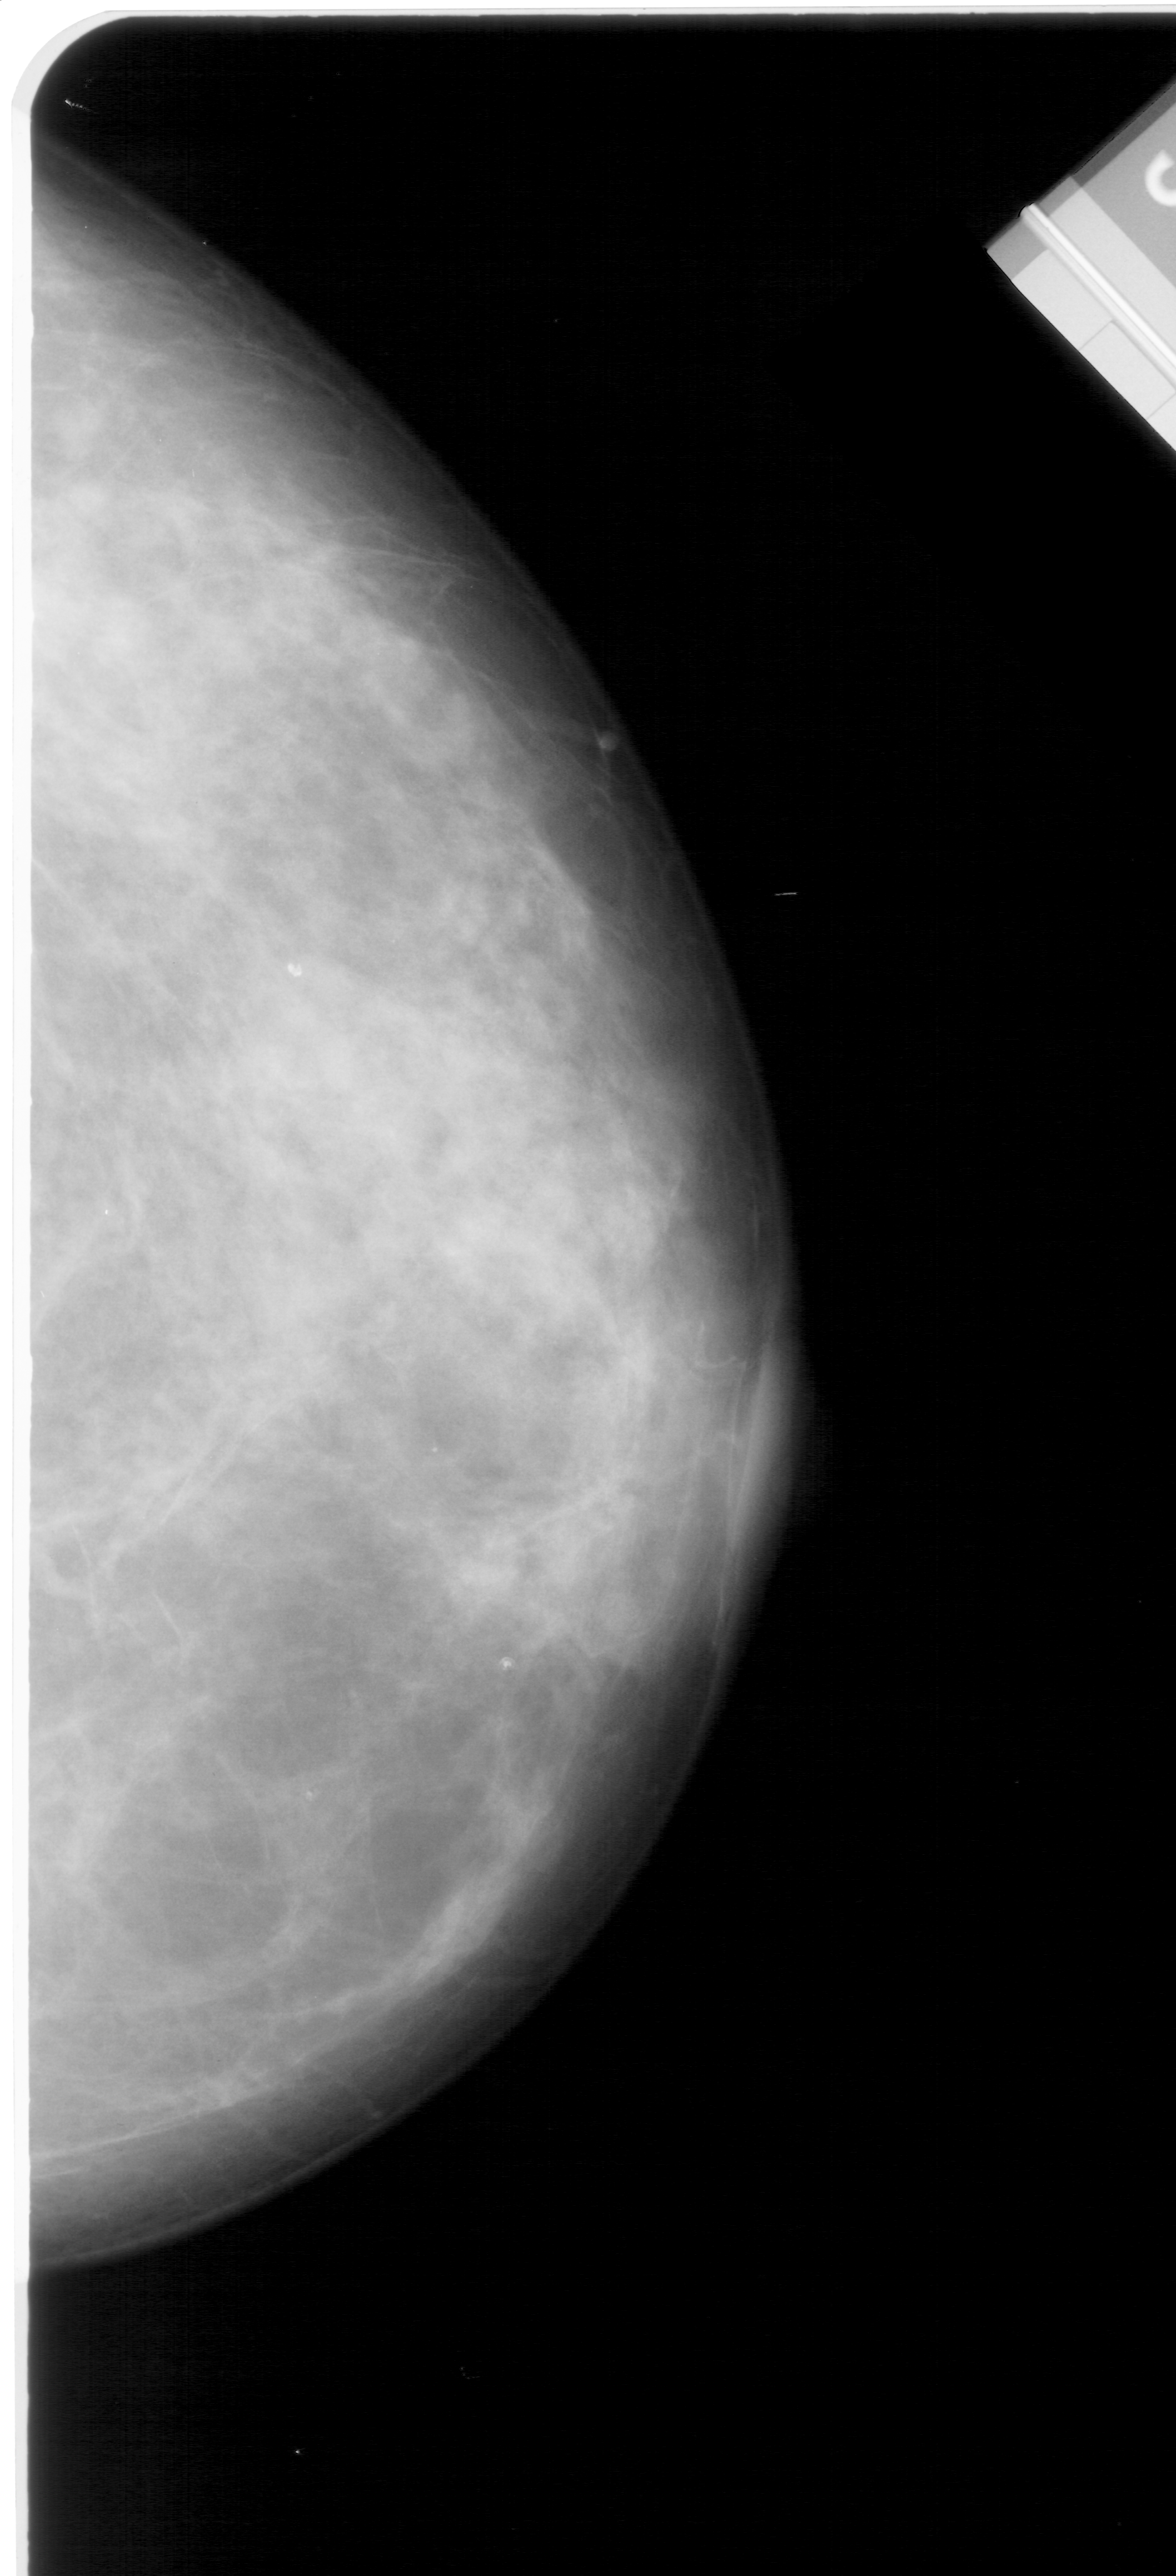
Digitized screen-film mammogram; right breast; CC view; breast composition: extremely dense (BI-RADS density category 4 of 4).
Marked abnormality: mass, shape irregular, margins ill defined; BI-RADS assessment category 4; pathology result (as recorded, not read from the image): benign.